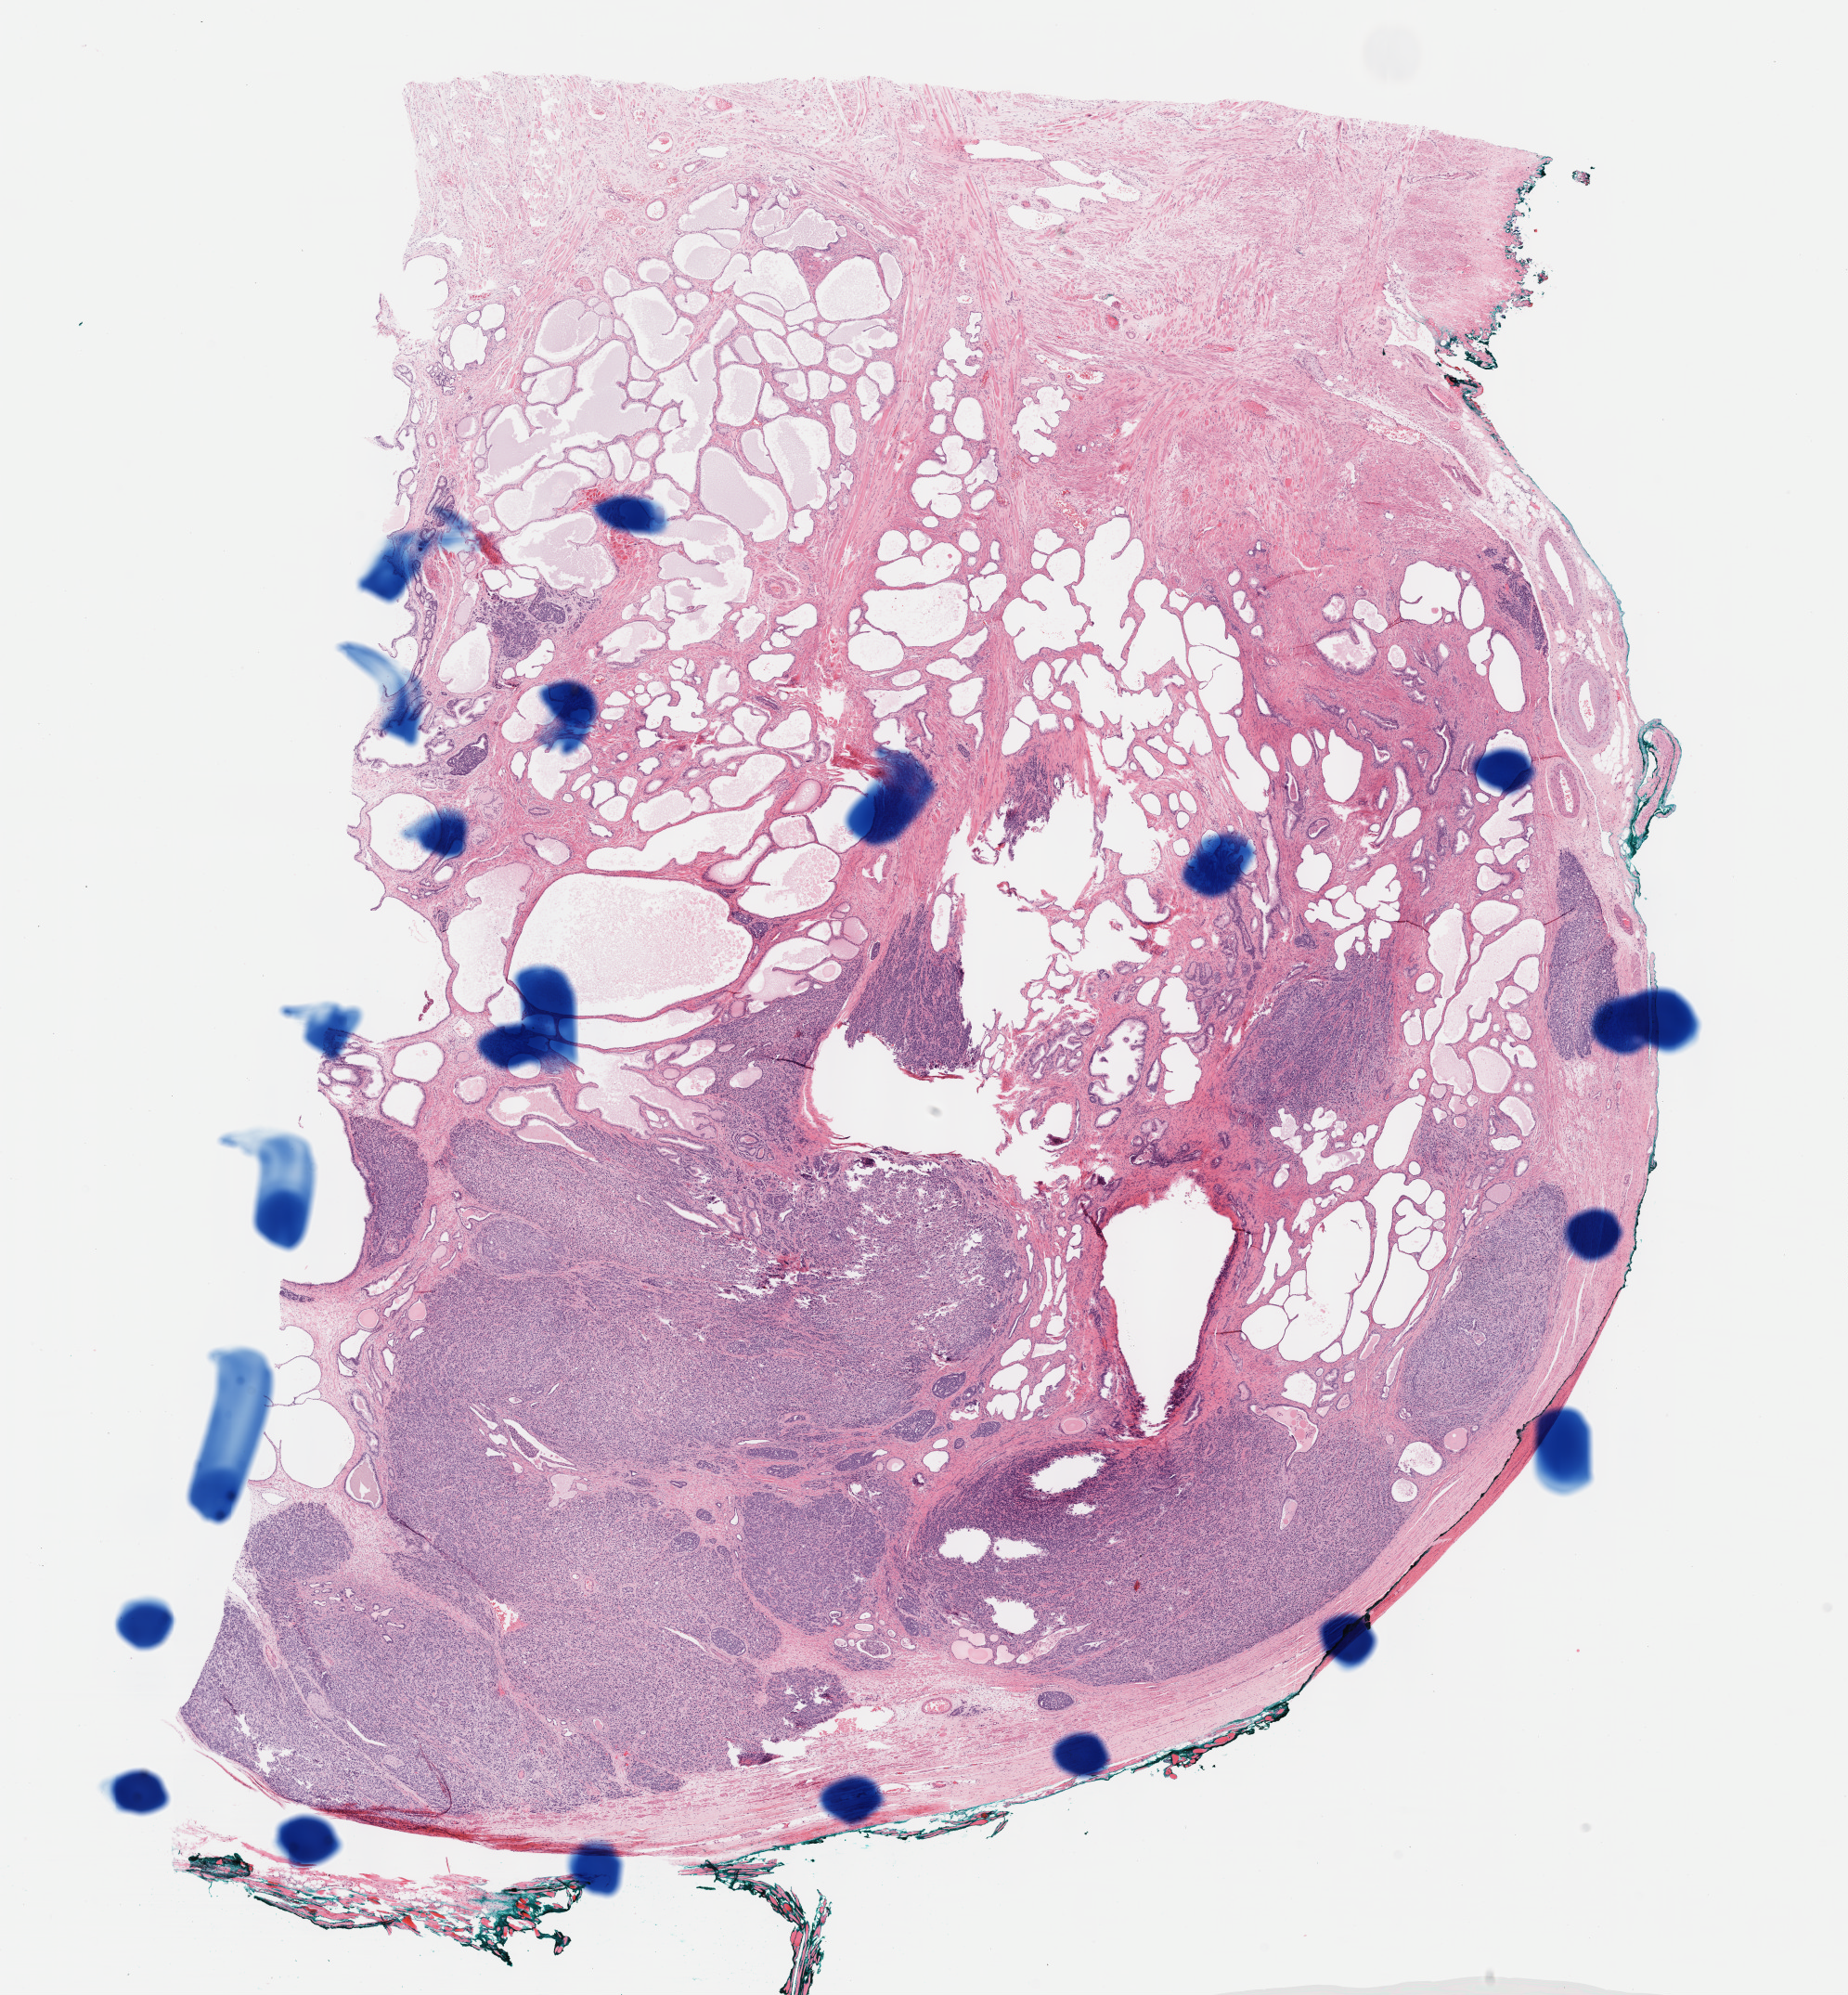
H&E whole-slide image — whole scanned area (about 16.1 x 17.4 mm, from a 40x scan) shown as a low-resolution overview. FFPE section. Sample: primary tumour, prostate. Male, age 68 years at initial diagnosis. Gleason score: 9 (4+5).
Lymph nodes positive (case pathology): 0 of 10 examined. Diagnosis: Adenocarcinoma, NOS (prostate gland).